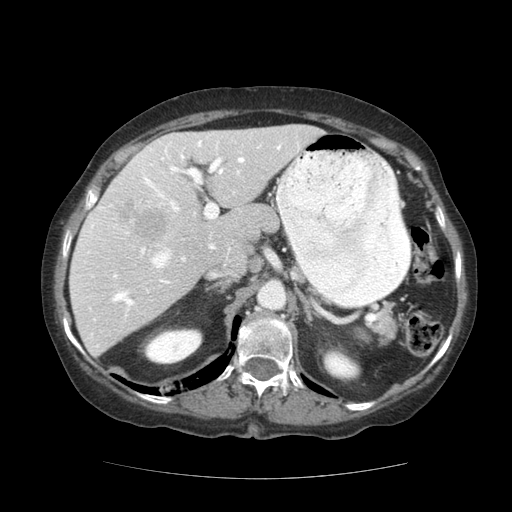
Contrast-enhanced abdominal CT (liver protocol), one axial slice; slice 76 of 111 in the series (ordered by position); 140 kVp; soft-tissue window (W 400 / L 40 HU); 2.5 mm slice thickness; 512 × 512 image matrix, field of view 360 × 360 mm. Case-level facts recorded for this patient, not image findings: diagnosis: hepatocellular carcinoma (patient treated with transarterial chemoembolisation; whether this scan precedes or follows treatment is not stated here); TNM stage (as recorded): Stage-I; Child-Pugh class: A; tumour differentiation: moderately-poorly differentiated; tumour nodularity: uninodular.
Structures marked on this image (semi-automatically segmented with operator editing):
- liver parenchyma outside the tumour (the mass and vessels are separate outlines, so this box may not span the whole liver): bounding box [x1, y1, x2, y2] px = [69, 124, 324, 356]
- mass: [121, 202, 168, 243]
- liver vessels: [88, 137, 299, 347]